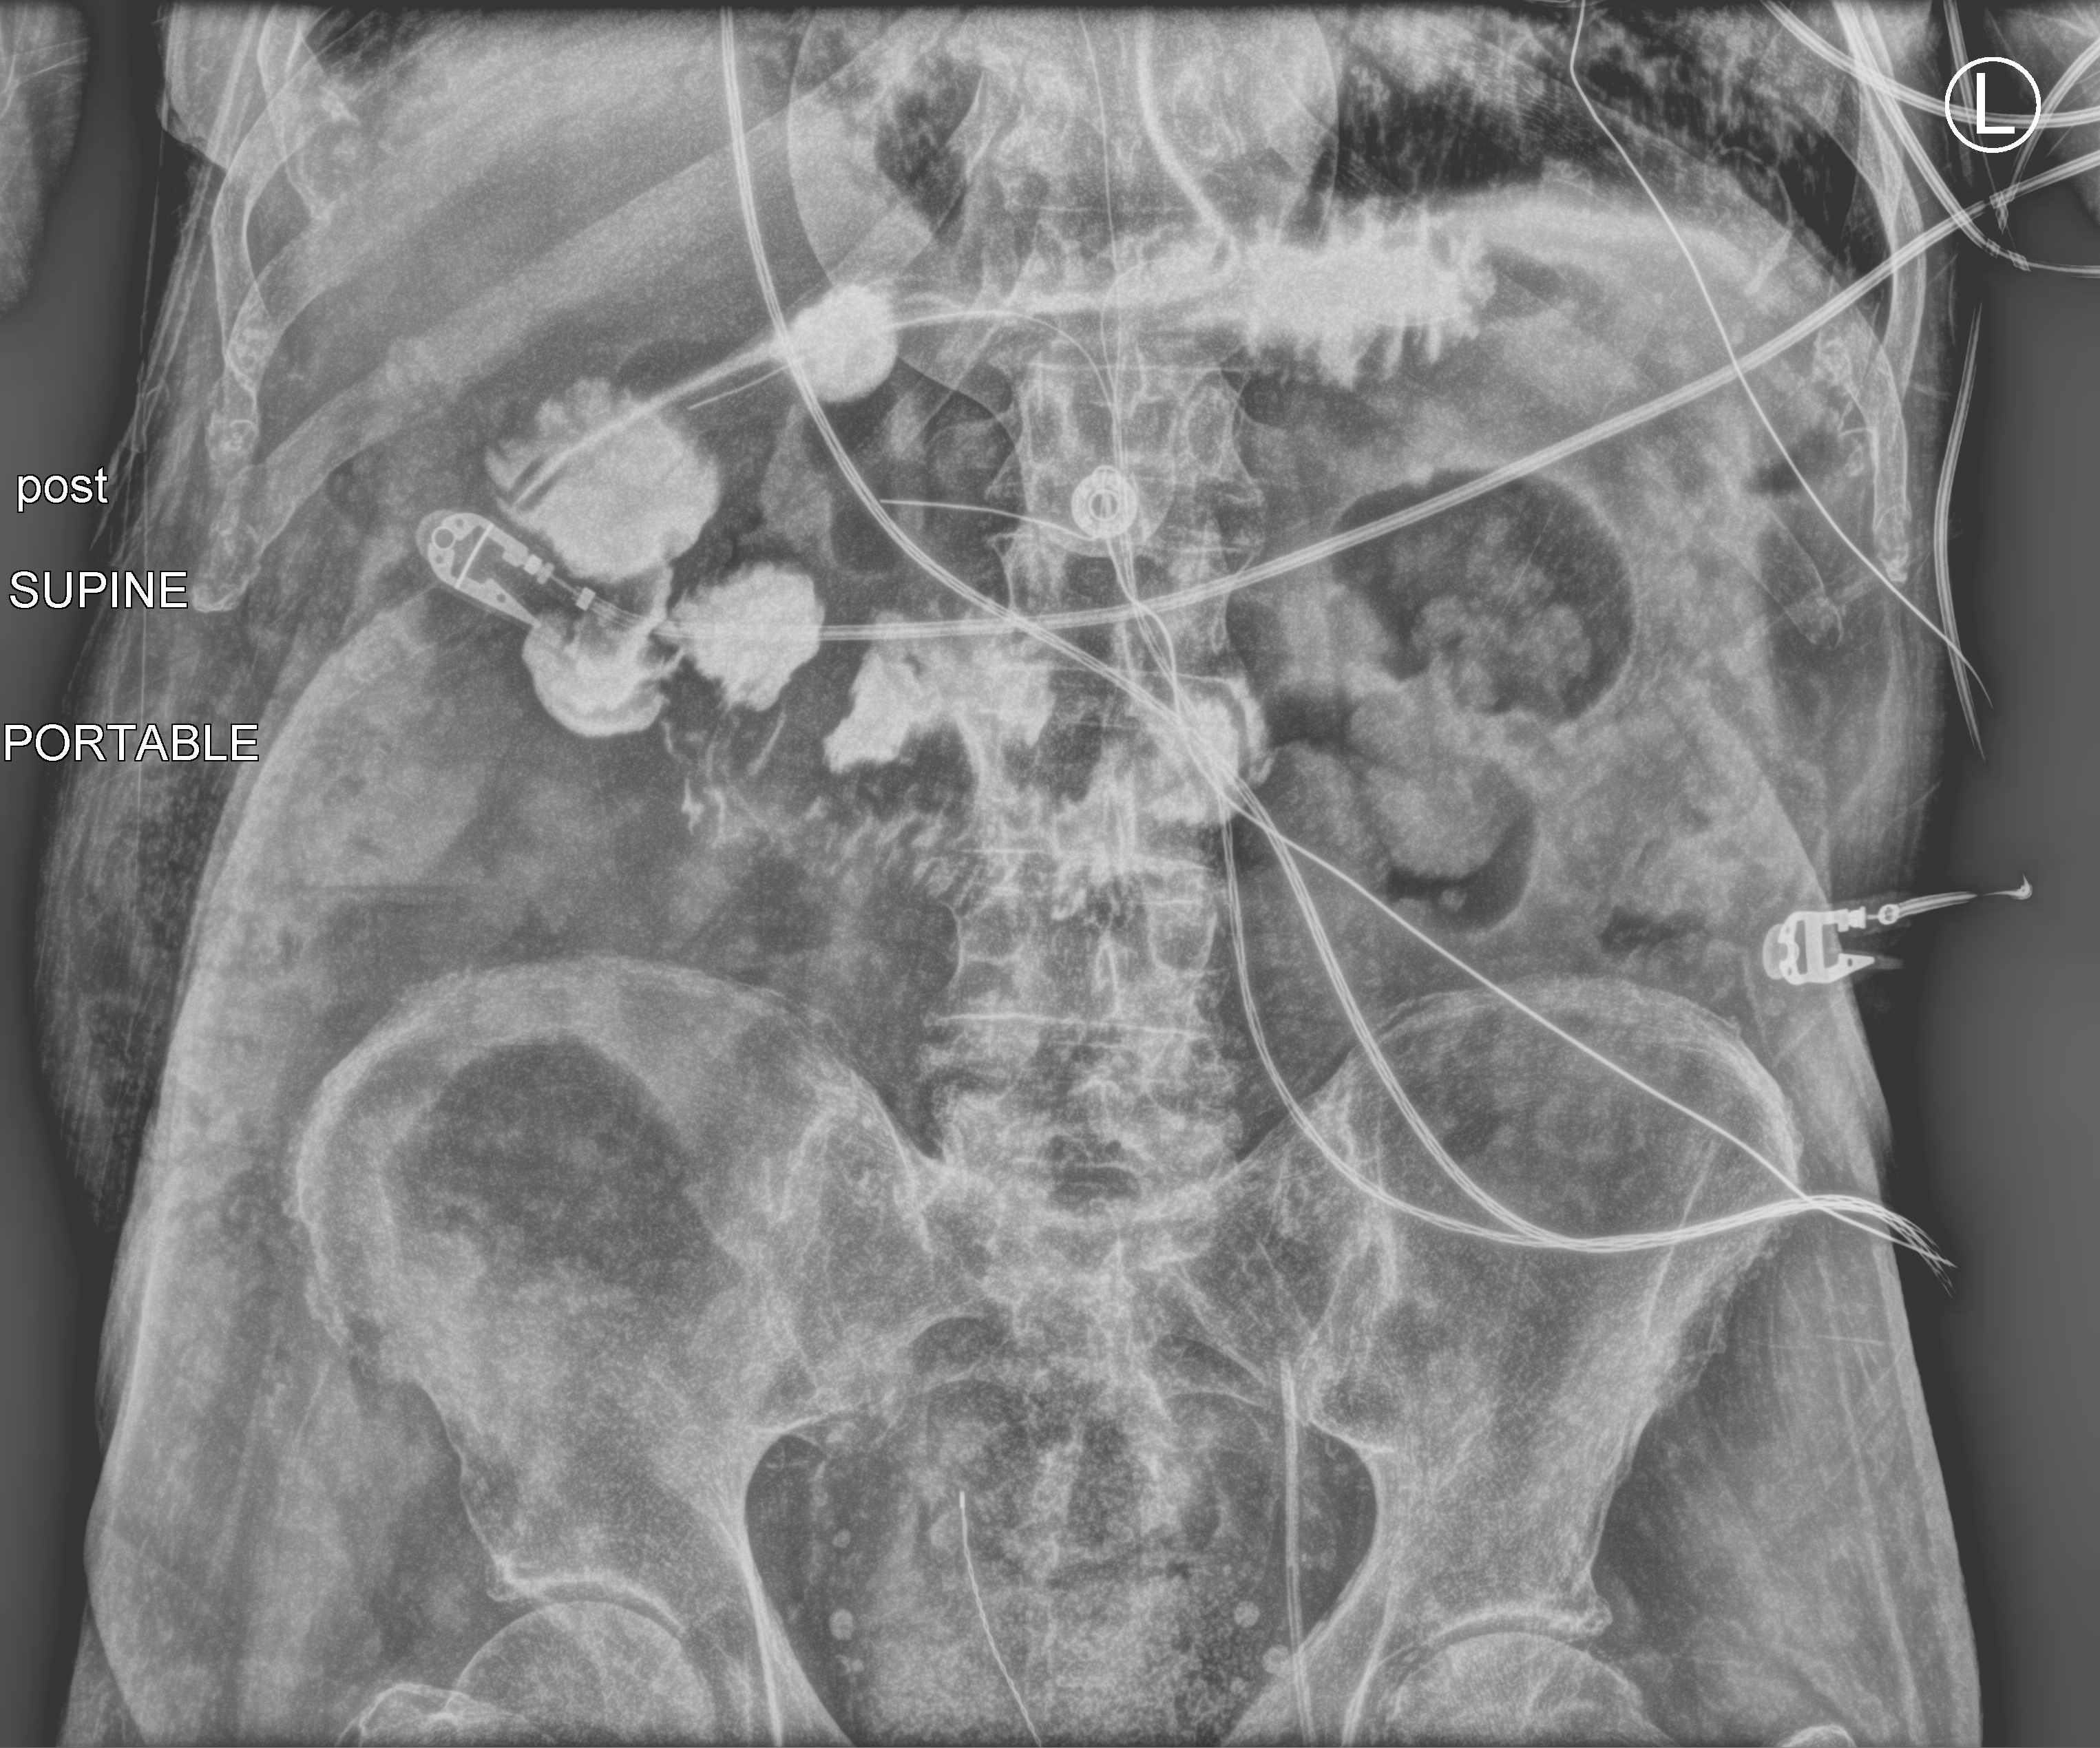
Bedside abdomen radiograph (computed radiography), anteroposterior (AP) projection. Patient hospitalised with COVID-19; male, aged 75–90 years.
Hospital-stay facts (about this admission, not read from this image; timing relative to this image not recorded): mechanically ventilated during this hospital stay: yes.